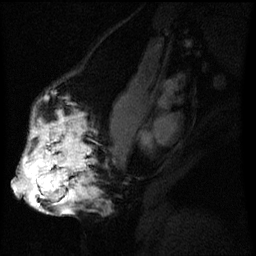
Breast MRI (dynamic contrast-enhanced), one sagittal slice. Position 27 of 60 along the scan axis. Dynamic contrast-enhanced series, image 2 of 3 at this slice position (ordered by acquisition). 1.5 T. TE 4.2 ms, TR 8 ms. 256 × 256 image matrix, field of view 200 × 200 mm. Female patient, age 50 years.
Annotated regions visible in this slice (semi-automatically segmented with operator editing):
- analysis volume of interest (the breast-tissue region the enhancement analysis was run in; not a lesion): bounding box <19,112,95,211> (left, top, right, bottom; pixels)
- tumour enhancement mask (voxels above the 70 % enhancement threshold inside the analysis volume of interest): <19,116,87,211>